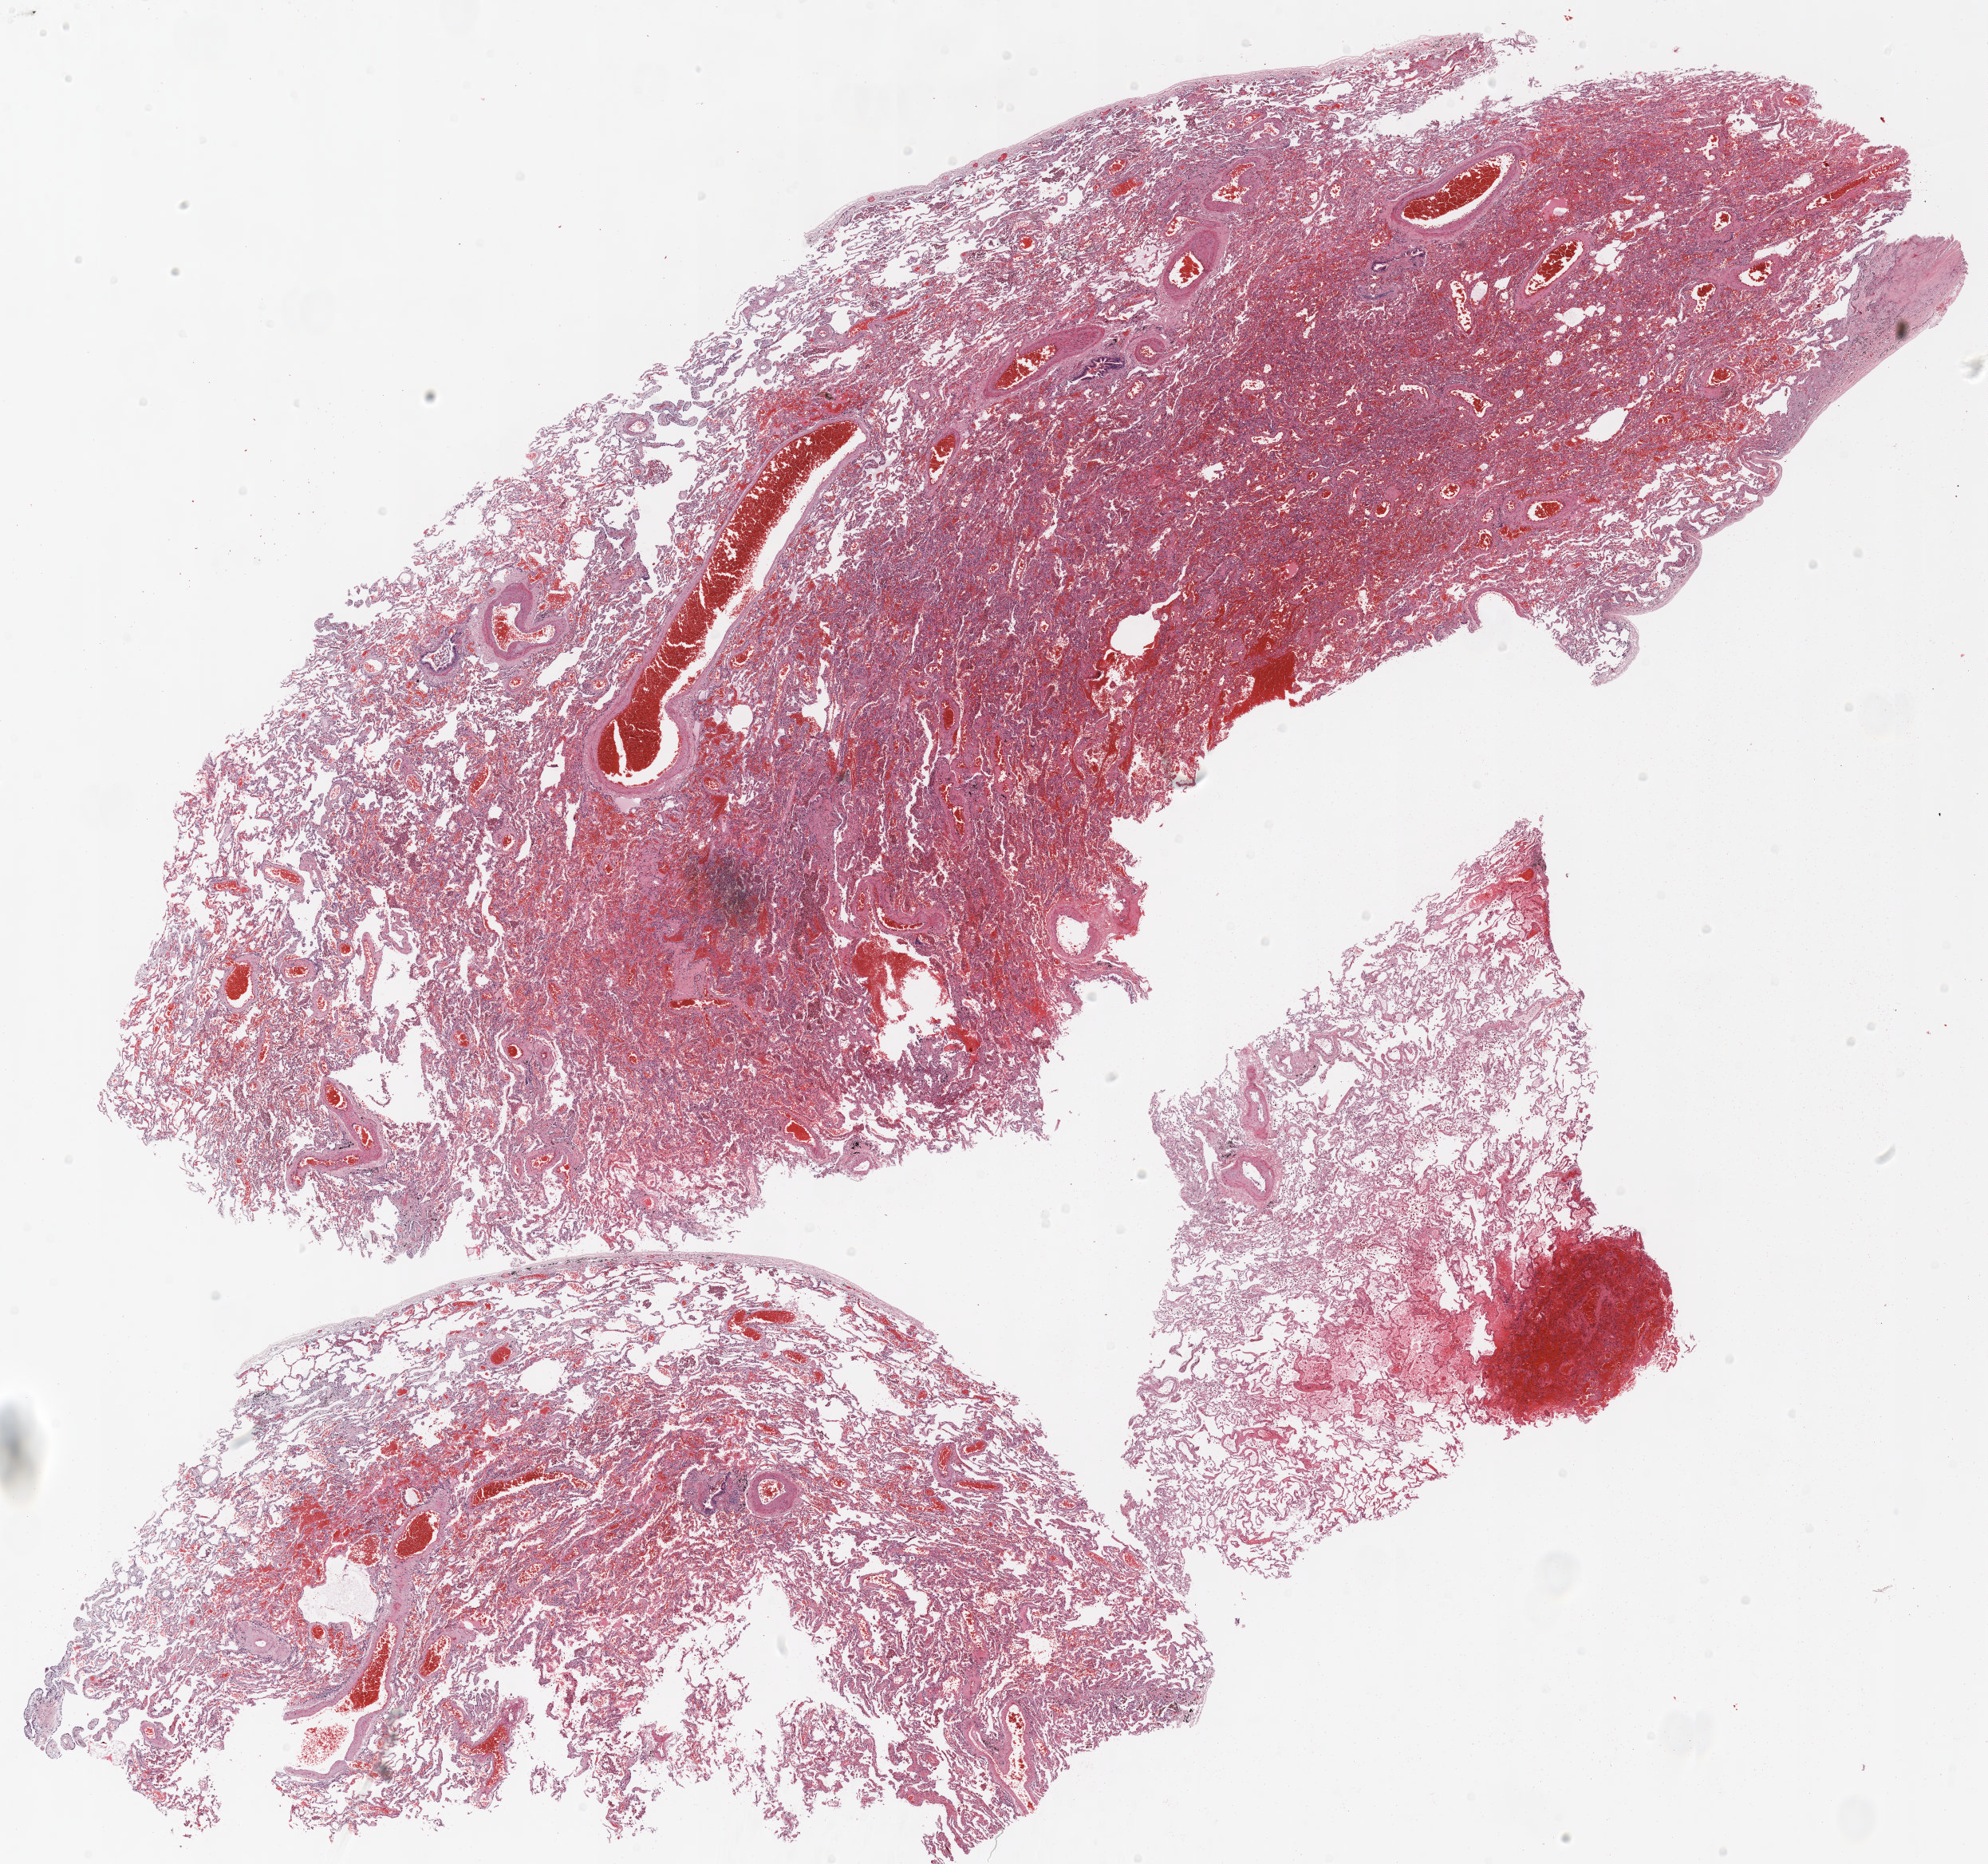
H&E-stained whole-slide image, low-resolution overview of the scanned area, about 20.0 x 18.8 mm (from a 20x scan). Formalin-fixed paraffin-embedded (FFPE) section. Lung. Male patient, aged 69 at enrolment. Former smoker at enrolment. Grade: poorly differentiated (G3).
Participant's lung-cancer diagnosis: Large cell neuroendocrine carcinoma (ICD-O-3 8013/3). Stage (AJCC 6th edition): IA. ICD-O-3 topography: upper lobe of lung (C34.1). Primary tumour location (clinical record): right upper lobe. Tumour size (pathology): 23 mm.